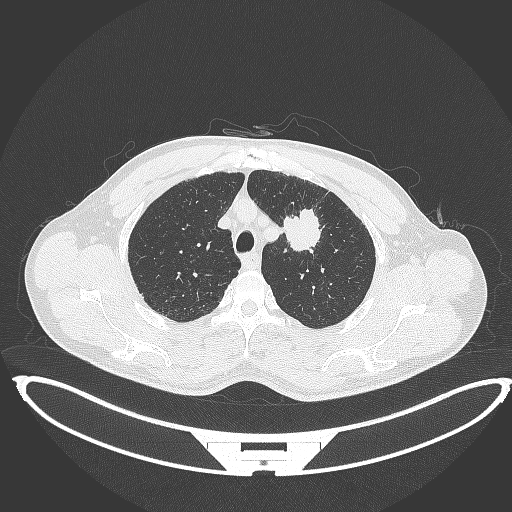
Chest CT, one axial slice. Slice 352 of 395 in the series (ordered by position). 120 kVp. Lung window (W 1500 / L -600 HU). 1 mm slice thickness. 512 × 512 image matrix, field of view 457 × 457 mm. Male patient, age 60 years. Case-level facts recorded for this patient, not image findings: clinical TNM (as recorded): T2a N0 M0; histopathological grade: G1-G2.
Structures marked on this image (rectangle marked by the reading radiologist):
- lung tumour (recorded histology: squamous cell carcinoma): box from (x=281, y=204) to (x=324, y=255) px